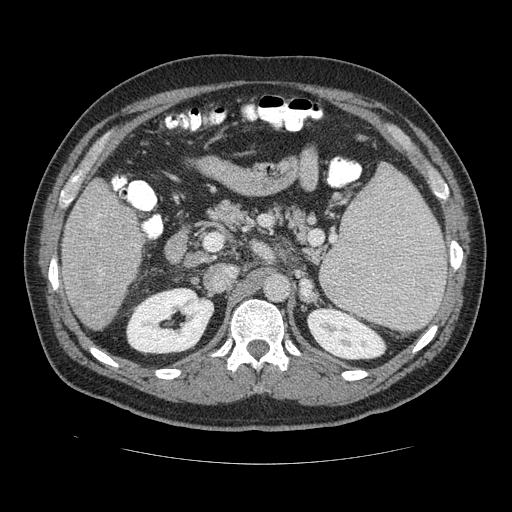
Contrast-enhanced abdominal CT (liver protocol), one axial slice; slice 66 of 113 in the series (ordered by position); 120 kVp; soft-tissue window (W 400 / L 40 HU); 2.5 mm slice thickness; 512 × 512 image matrix, field of view 400 × 400 mm. Case-level facts recorded for this patient, not image findings: diagnosis: hepatocellular carcinoma (patient treated with transarterial chemoembolisation; whether this scan precedes or follows treatment is not stated here); TNM stage (as recorded): Stage-II; Child-Pugh class: B; tumour differentiation: moderately differentiated; tumour nodularity: multinodular.
Annotated regions visible in this slice (semi-automatic segmentation, software-assisted and operator-edited):
- liver parenchyma outside the tumour (the mass and vessels are separate outlines, so this box may not span the whole liver): bounding box (x1, y1, x2, y2) in pixels: (60, 178, 148, 332)
- liver vessels: (93, 218, 139, 277)